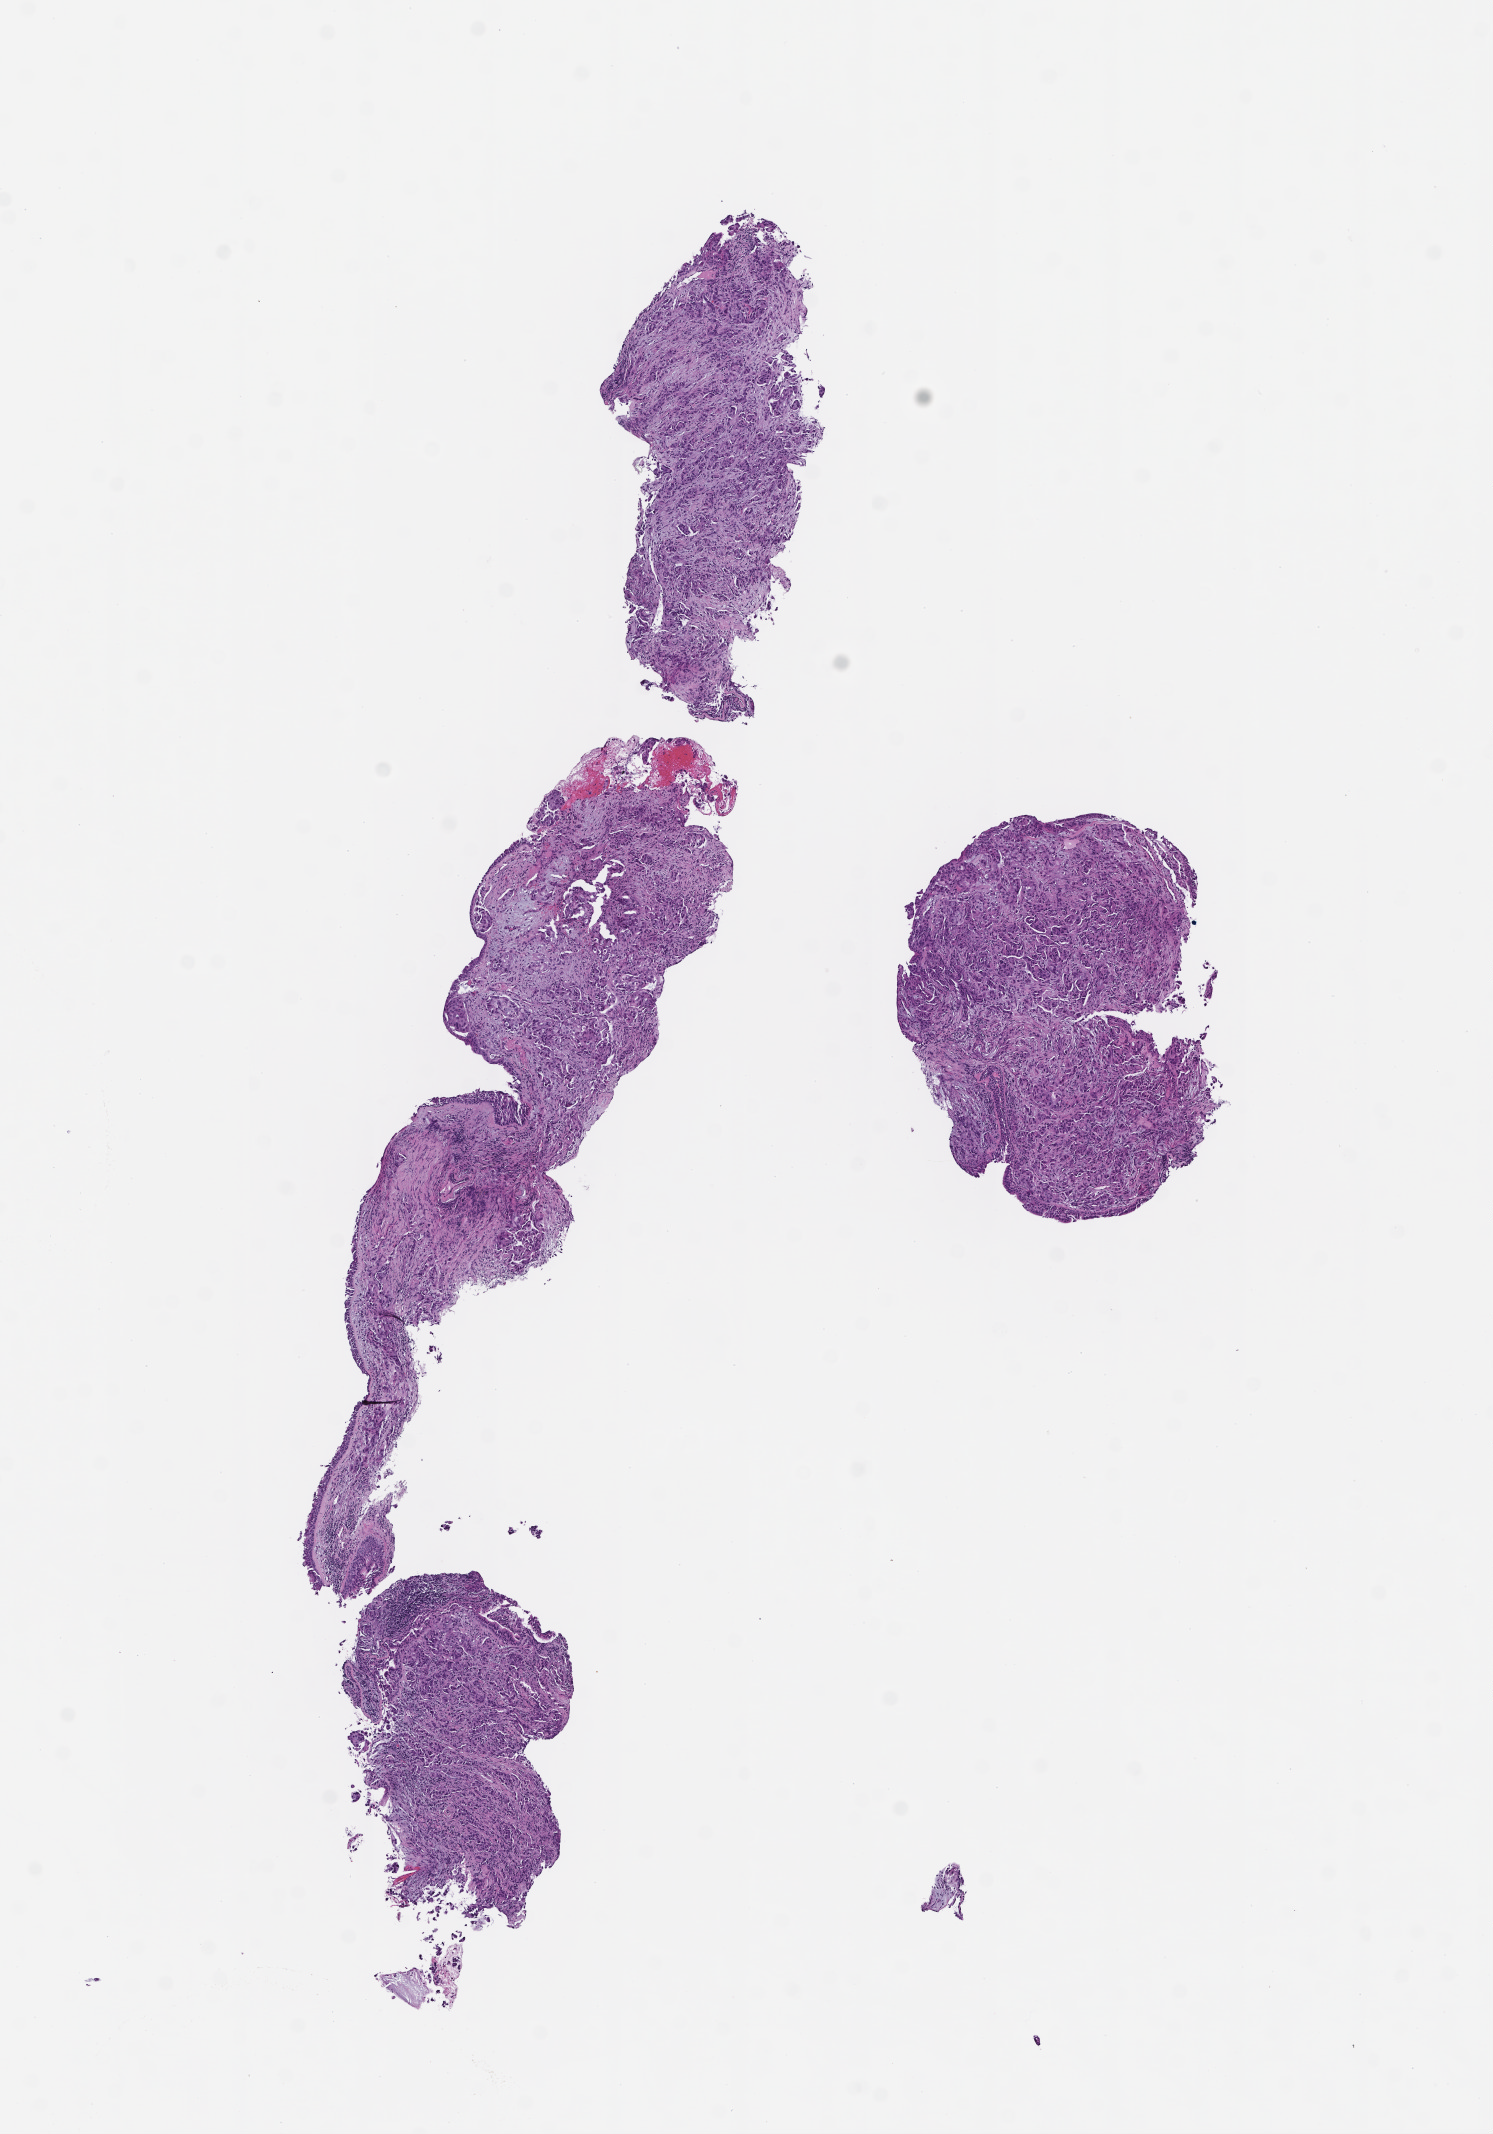
Digitized H&E-stained section — whole scanned area (about 6.0 x 8.6 mm) shown as a low-resolution overview, FFPE section, tissue site: lung. Female patient.
This section: primary tumor. Diagnosis: Non-Small Cell Lung Carcinoma.